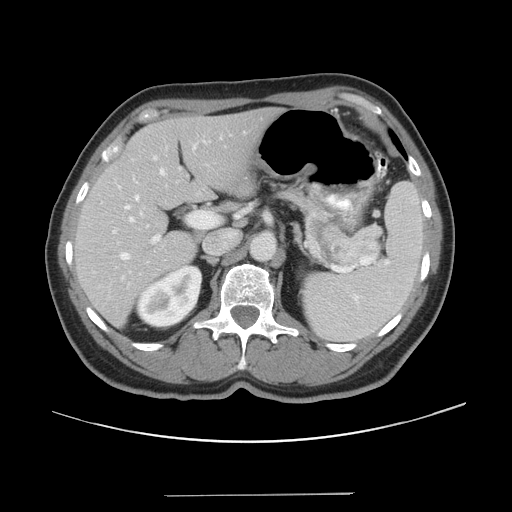
Contrast-enhanced abdominal CT, one axial slice; slice 24 of 43 in the series (ordered by position); intravenous contrast given; soft-tissue window (W 400 / L 40 HU); 5 mm slice thickness; 512 × 512 image matrix. Male patient, age 65 years. From the clinical record (not read from this slice): diagnosis: colorectal cancer liver metastases, imaged before liver resection; multiple liver metastases: no; largest metastasis: 3.8 cm.
Outlined on this slice (outlined manually by an expert reader):
- hepatic veins: box from (x=121, y=159) to (x=167, y=263) px
- liver: (x=75, y=108)–(x=278, y=324)
- planned liver remnant (the part of the liver to remain after resection): (x=75, y=108)–(x=278, y=324)
- portal vein (with intrahepatic branches): (x=113, y=134)–(x=231, y=248)